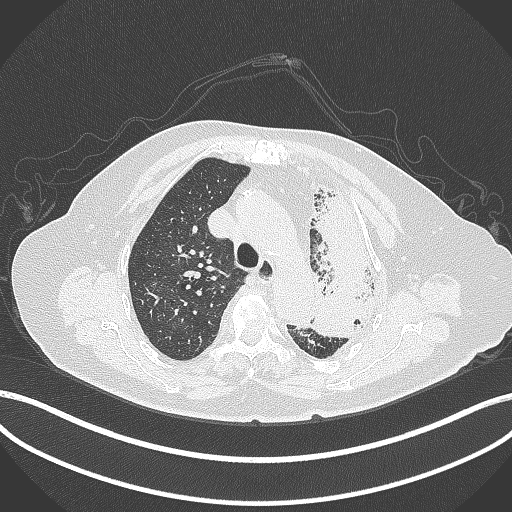
Chest CT, one axial slice. Slice 291 of 399 in the series (ordered by position). Reconstruction kernel B70f. 120 kVp. Lung window (W 1500 / L -600 HU). 1 mm slice thickness. 512 × 512 image matrix, field of view 400 × 400 mm. Female patient, age 75 years. Case-level facts recorded for this patient, not image findings: clinical TNM (as recorded): T3 N3 M1.
Annotated regions visible in this slice (rectangle marked by the reading radiologist):
- lung tumour (recorded histology: adenocarcinoma): bounding box [x1, y1, x2, y2] px = [298, 190, 377, 339]